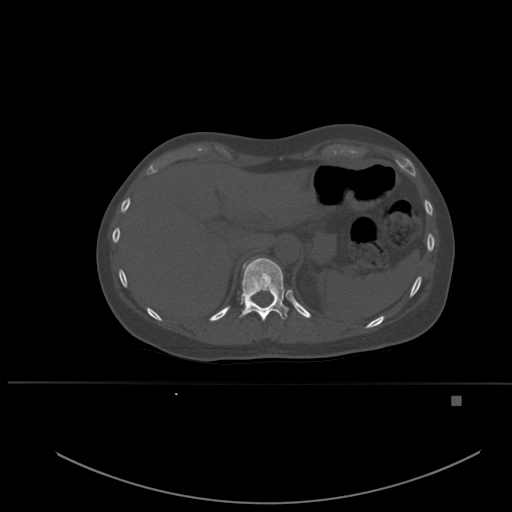
CT including the spine, one axial slice. Position 272 of 651 along the scan axis. Bone window (W 1800 / L 400 HU). 1.5 mm slice thickness. 512 × 512 image matrix, field of view 443 × 443 mm. Female patient, age 49 years. Case-level facts recorded for this patient, not image findings: primary cancer: breast.
Annotated regions visible in this slice (semi-automatically segmented with operator editing):
- T11 vertebra: bounding box <239,257,289,321> (left, top, right, bottom; pixels)